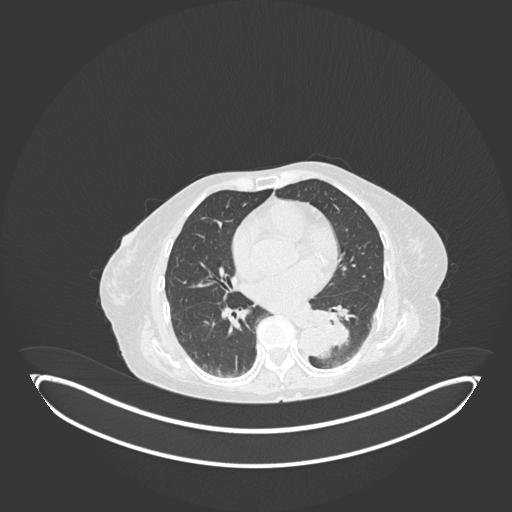
Chest CT, one axial slice. Slice 51 of 189 in the series (ordered by position). Reconstruction kernel B30f. Lung window (W 1500 / L -600 HU). 1 mm slice thickness. 512 × 512 image matrix, field of view 500 × 500 mm. Patient: female, 82 years. Case-level facts recorded for this patient, not image findings: clinical TNM (as recorded): T1b N0 M1.
Annotated regions visible in this slice (rectangle marked by the reading radiologist):
- lung tumour (recorded histology: adenocarcinoma): bounding box <312,312,354,353> (left, top, right, bottom; pixels)